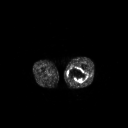
FDG PET of an extremity soft-tissue mass (from a PET/CT study), one axial slice. Slice 225 of 267 in the series (ordered by position). 3.27 mm slice thickness. 128 × 128 image matrix. Male patient, age 44 years. Case-level facts recorded for this patient, not image findings: histological type: undifferentiated pleomorphic liposarcoma; grade: high; site of the primary tumour: left thigh.
Outlined on this slice (expert contour drawn on MRI and transferred to this co-registered scan by the dataset authors):
- gross tumour volume including surrounding oedema: bounding box (x1, y1, x2, y2) in pixels: (67, 67, 87, 83)
- gross tumour volume (mass): (68, 67, 87, 83)